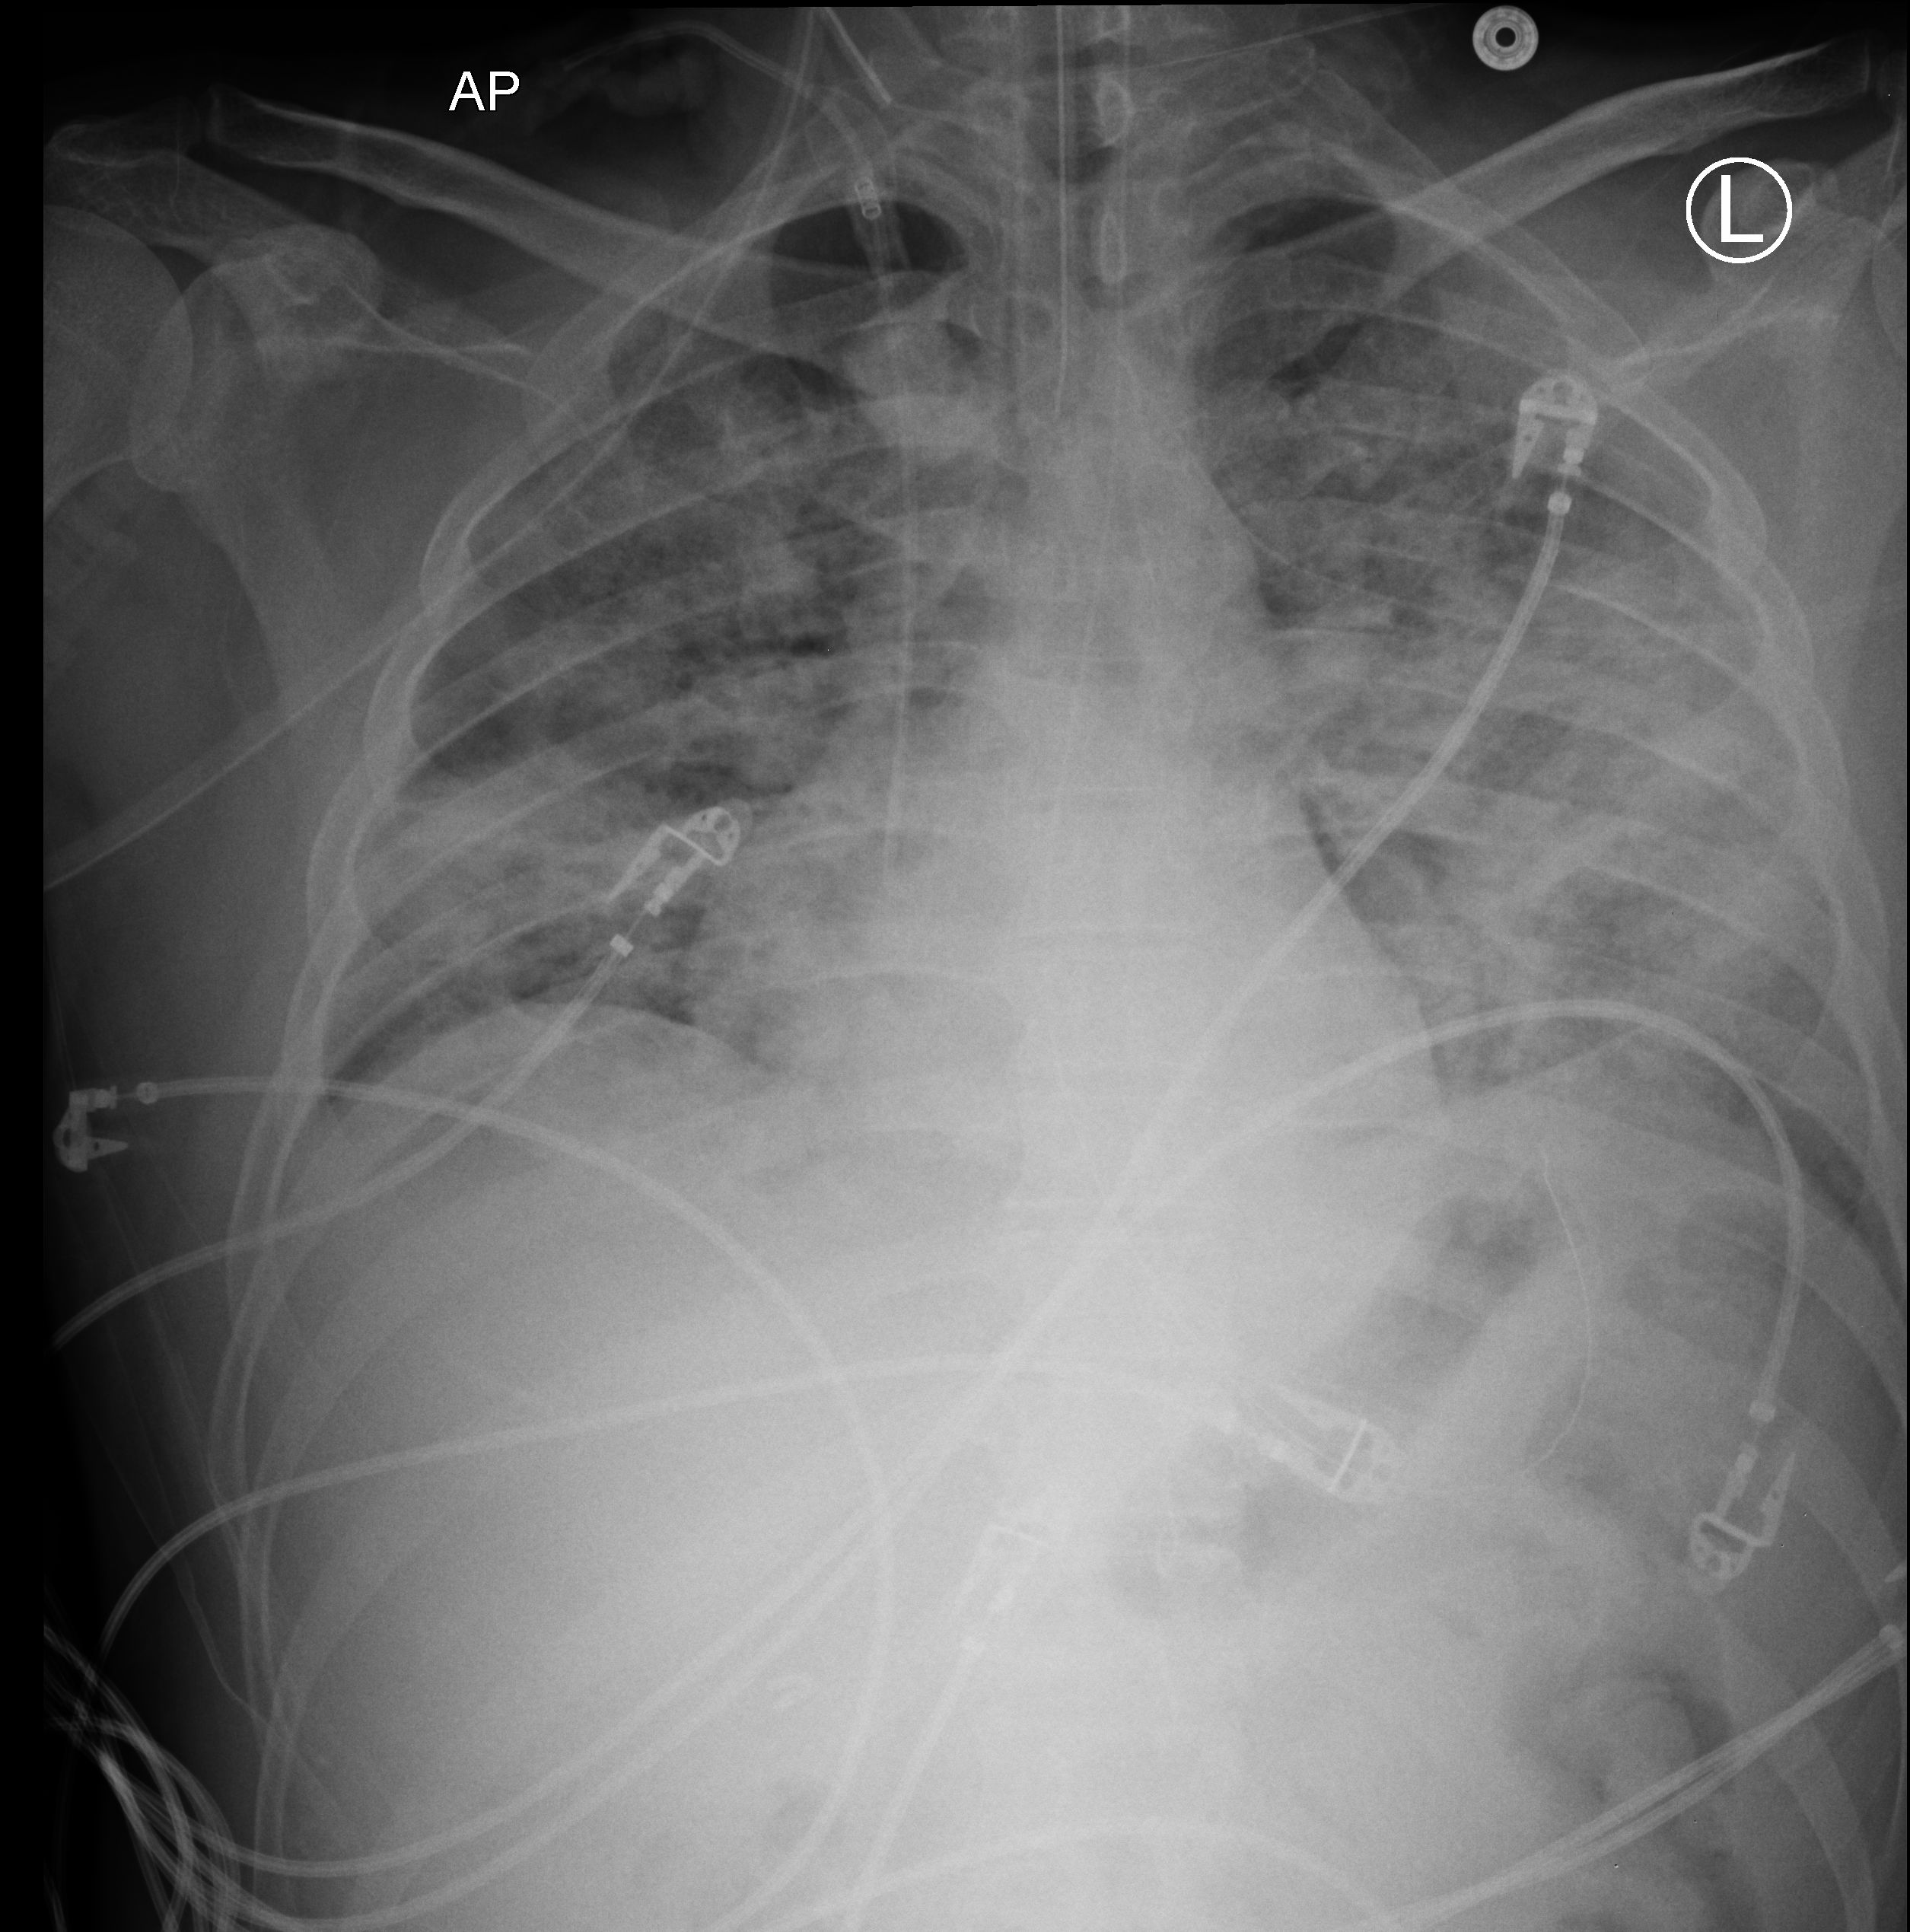
Chest X-ray (portable), anteroposterior (AP) projection. Male patient hospitalised with COVID-19, age 18–59 years.
Admission-level facts for this patient (not findings on this image; timing relative to this image not recorded):
- length of hospital stay: 29 days
- mechanically ventilated during this hospital stay: yes
- admitted to intensive care during this hospital stay: yes